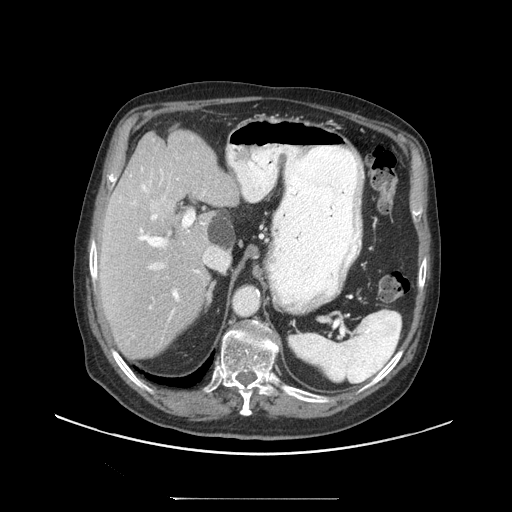
Contrast-enhanced abdominal CT (liver protocol), one axial slice; slice 66 of 97 in the series (ordered by position); reconstruction kernel STANDARD; soft-tissue window (W 400 / L 40 HU); 512 × 512 image matrix, field of view 450 × 450 mm. Case-level facts recorded for this patient, not image findings: diagnosis: hepatocellular carcinoma (patient treated with transarterial chemoembolisation; whether this scan precedes or follows treatment is not stated here); TNM stage (as recorded): Stage-IIIC.
Structures marked on this image (semi-automatically segmented with operator editing):
- liver parenchyma outside the tumour (the mass and vessels are separate outlines, so this box may not span the whole liver): bounding box (x1, y1, x2, y2) in pixels: (98, 130, 238, 360)
- liver vessels: (132, 169, 204, 320)